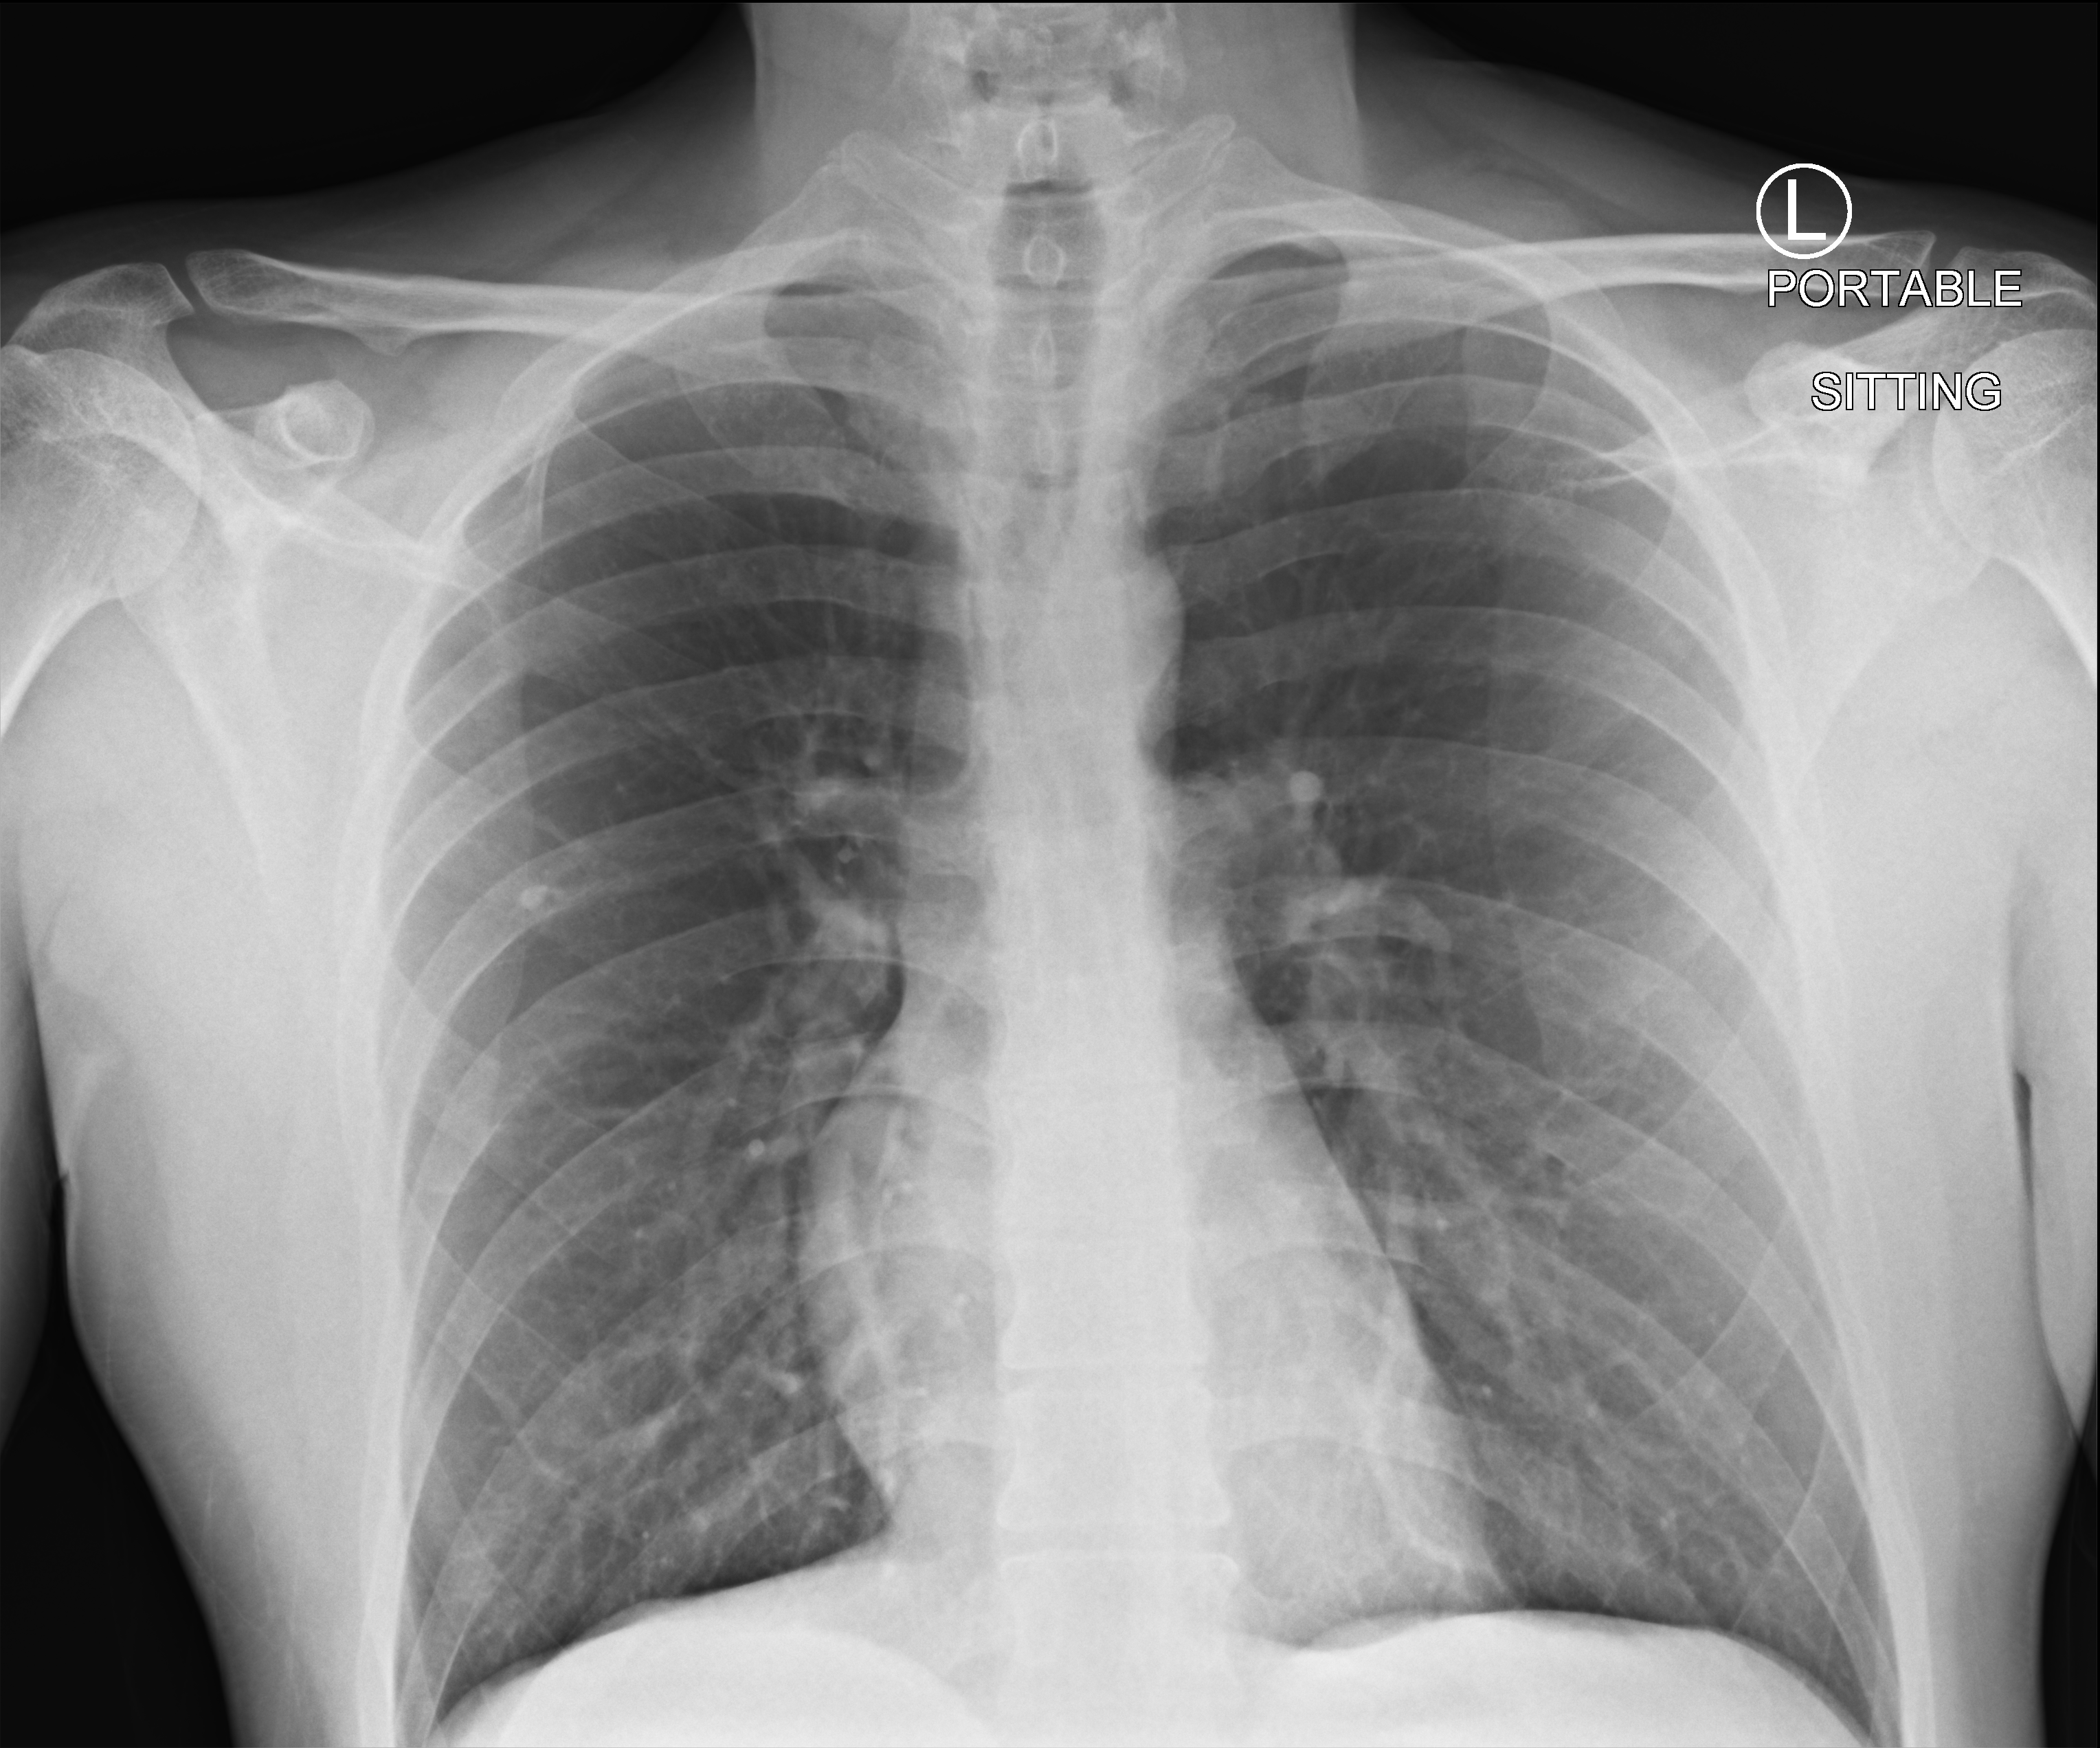
Bedside chest radiograph (computed radiography); anteroposterior (AP) projection. Male patient hospitalised with COVID-19, age 18–59 years.
Hospital-stay facts (about this admission, not read from this image; timing relative to this image not recorded): mechanically ventilated during this hospital stay: no.